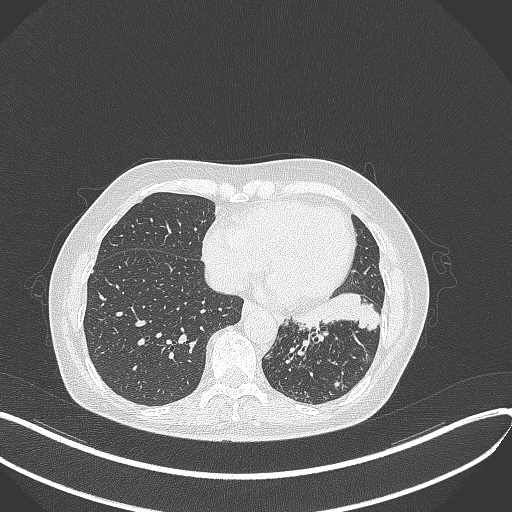
Chest CT, one axial slice. Position 134 of 429 along the scan axis. Lung window (W 1500 / L -600 HU). 512 × 512 image matrix, field of view 400 × 400 mm. Patient: female, 63 years. Case-level facts recorded for this patient, not image findings: clinical TNM (as recorded): T1b N0 M0; histopathological grade: G2-3.
Annotated regions visible in this slice (rectangle marked by the reading radiologist):
- lung tumour (recorded histology: adenocarcinoma): bounding box <289,291,380,337> (left, top, right, bottom; pixels)